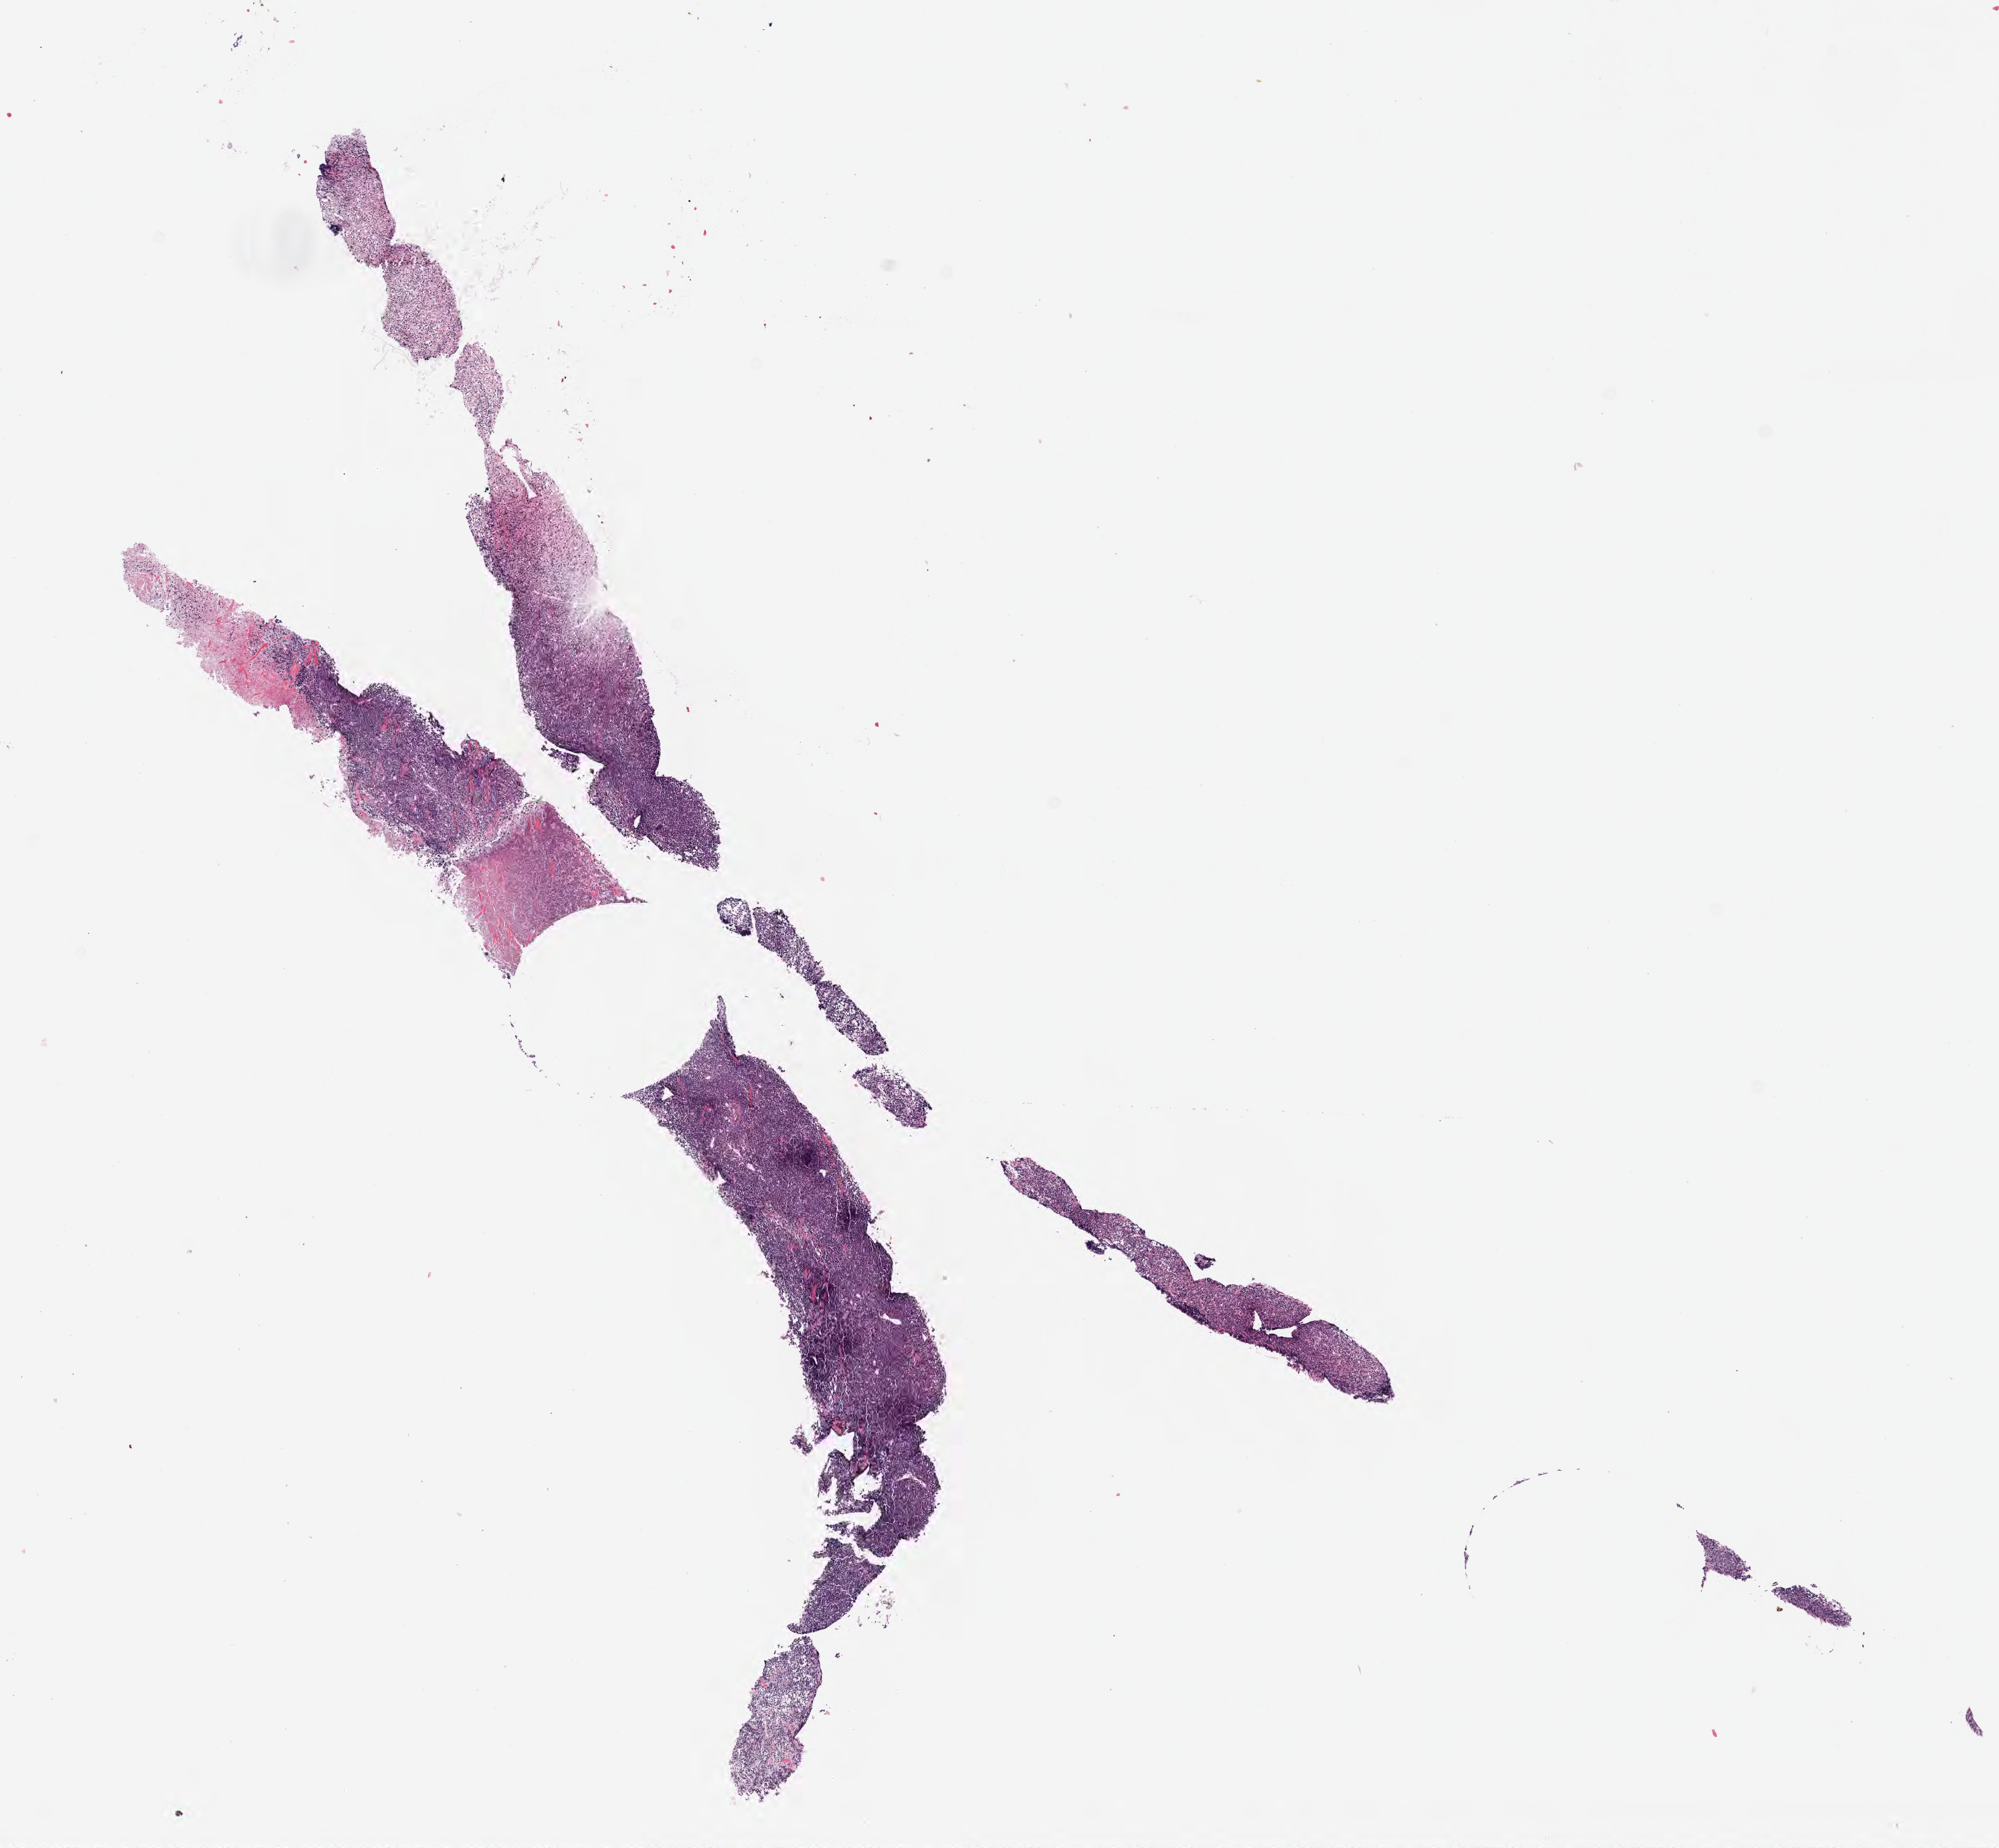
H&E whole-slide image — a low-resolution overview of the entire scanned area, about 12.1 x 11.2 mm; tumor tissue; site: abdomen proper. Patient male; age 14 years.
Diagnosis: Burkitt lymphoma, NOS.